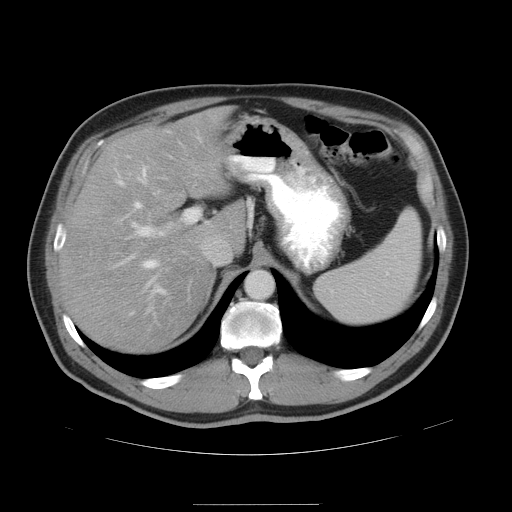
Contrast-enhanced abdominal CT, one axial slice. Position 33 of 47 along the scan axis. Intravenous contrast given. Soft-tissue window (W 400 / L 40 HU). 5 mm slice thickness. 512 × 512 image matrix, field of view 420 × 420 mm. Male patient, age 61 years. From the clinical record (not read from this slice): diagnosis: colorectal cancer liver metastases, imaged before liver resection; multiple liver metastases: no; largest metastasis: 1.2 cm; chemotherapy before resection: yes.
Annotated regions visible in this slice (manually delineated by an expert):
- hepatic veins: bounding box [x1, y1, x2, y2] px = [118, 167, 158, 285]
- liver: [62, 108, 246, 353]
- planned liver remnant (the part of the liver to remain after resection): [62, 108, 246, 353]
- portal vein (with intrahepatic branches): [119, 209, 200, 315]